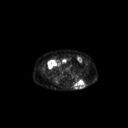
FDG PET of an extremity soft-tissue mass (from a PET/CT study), one axial slice; position 81 of 267 along the scan axis; 128 × 128 image matrix, field of view 700 × 700 mm. Male patient, age 69 years. Case-level facts recorded for this patient, not image findings: histological type: leiomyosarcoma; grade: intermediate; site of the primary tumour: left pelvis.
Outlined on this slice (expert contour drawn on MRI and transferred to this co-registered scan by the dataset authors):
- gross tumour volume (mass): box from (x=73, y=79) to (x=85, y=89) px